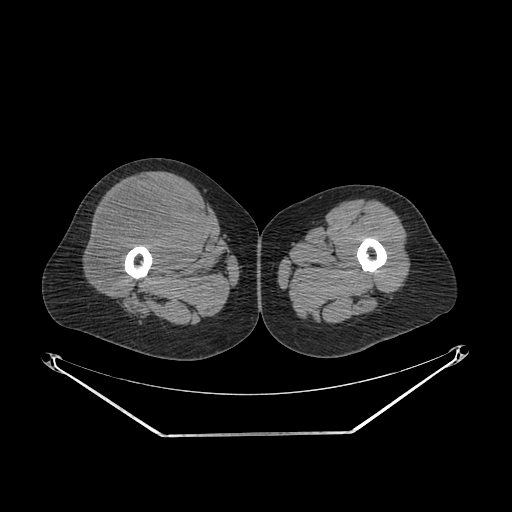
CT of an extremity soft-tissue mass (from a PET/CT study), one axial slice; position 250 of 311 along the scan axis; 140 kVp; soft-tissue window (W 400 / L 40 HU); 3.75 mm slice thickness; 512 × 512 image matrix, field of view 500 × 500 mm. Female patient. From the clinical record (not read from this slice): histological type: pleiomorphic undifferentiated sarcoma; grade: high; site of the primary tumour: right quadricep.
Outlined on this slice (expert contour drawn on MRI and transferred to this co-registered scan by the dataset authors):
- tumour plus oedema (research contour): box from (x=94, y=185) to (x=199, y=287) px
- tumour (research contour): (x=94, y=185)–(x=199, y=287)